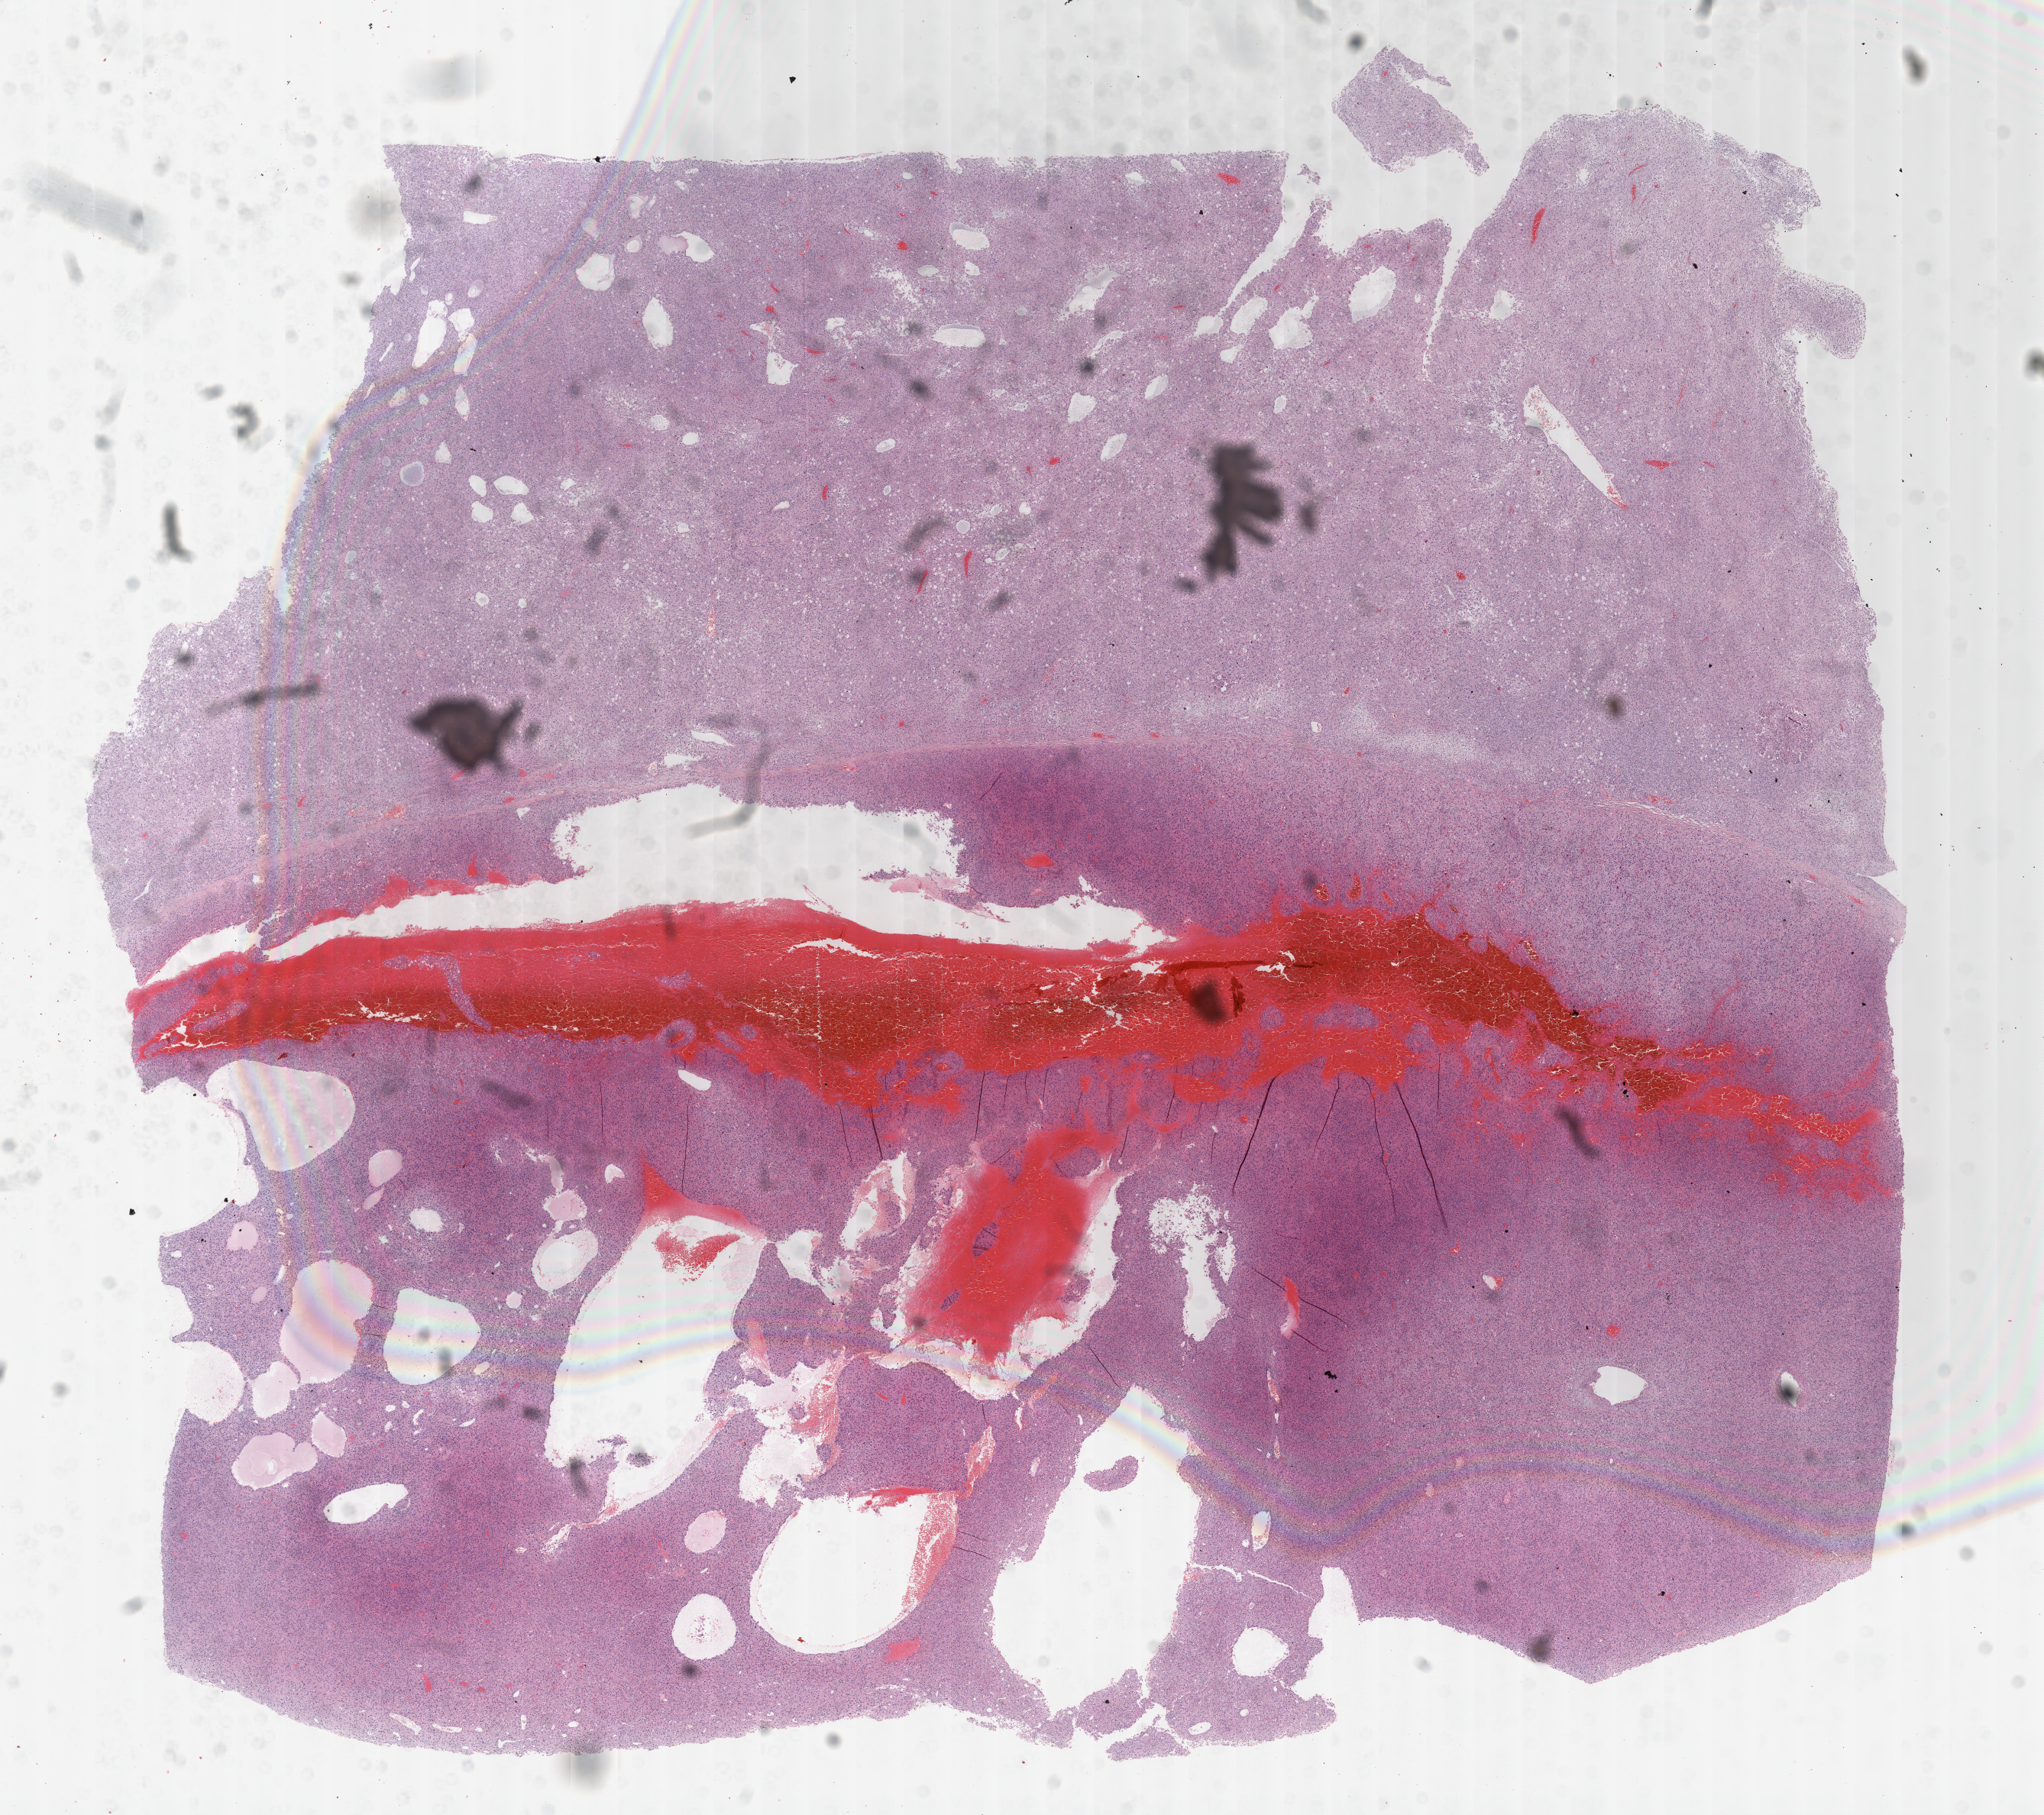
H&E-stained whole-slide image — shown as a low-resolution overview of the whole scanned area (about 21.6 x 19.2 mm, from a 40x scan); formalin-fixed paraffin-embedded (FFPE) diagnostic section; sample: primary tumour, adrenal cortex. Patient: male, age at initial diagnosis 40 years.
- diagnosis: Adrenal cortical carcinoma (cortex of adrenal gland)